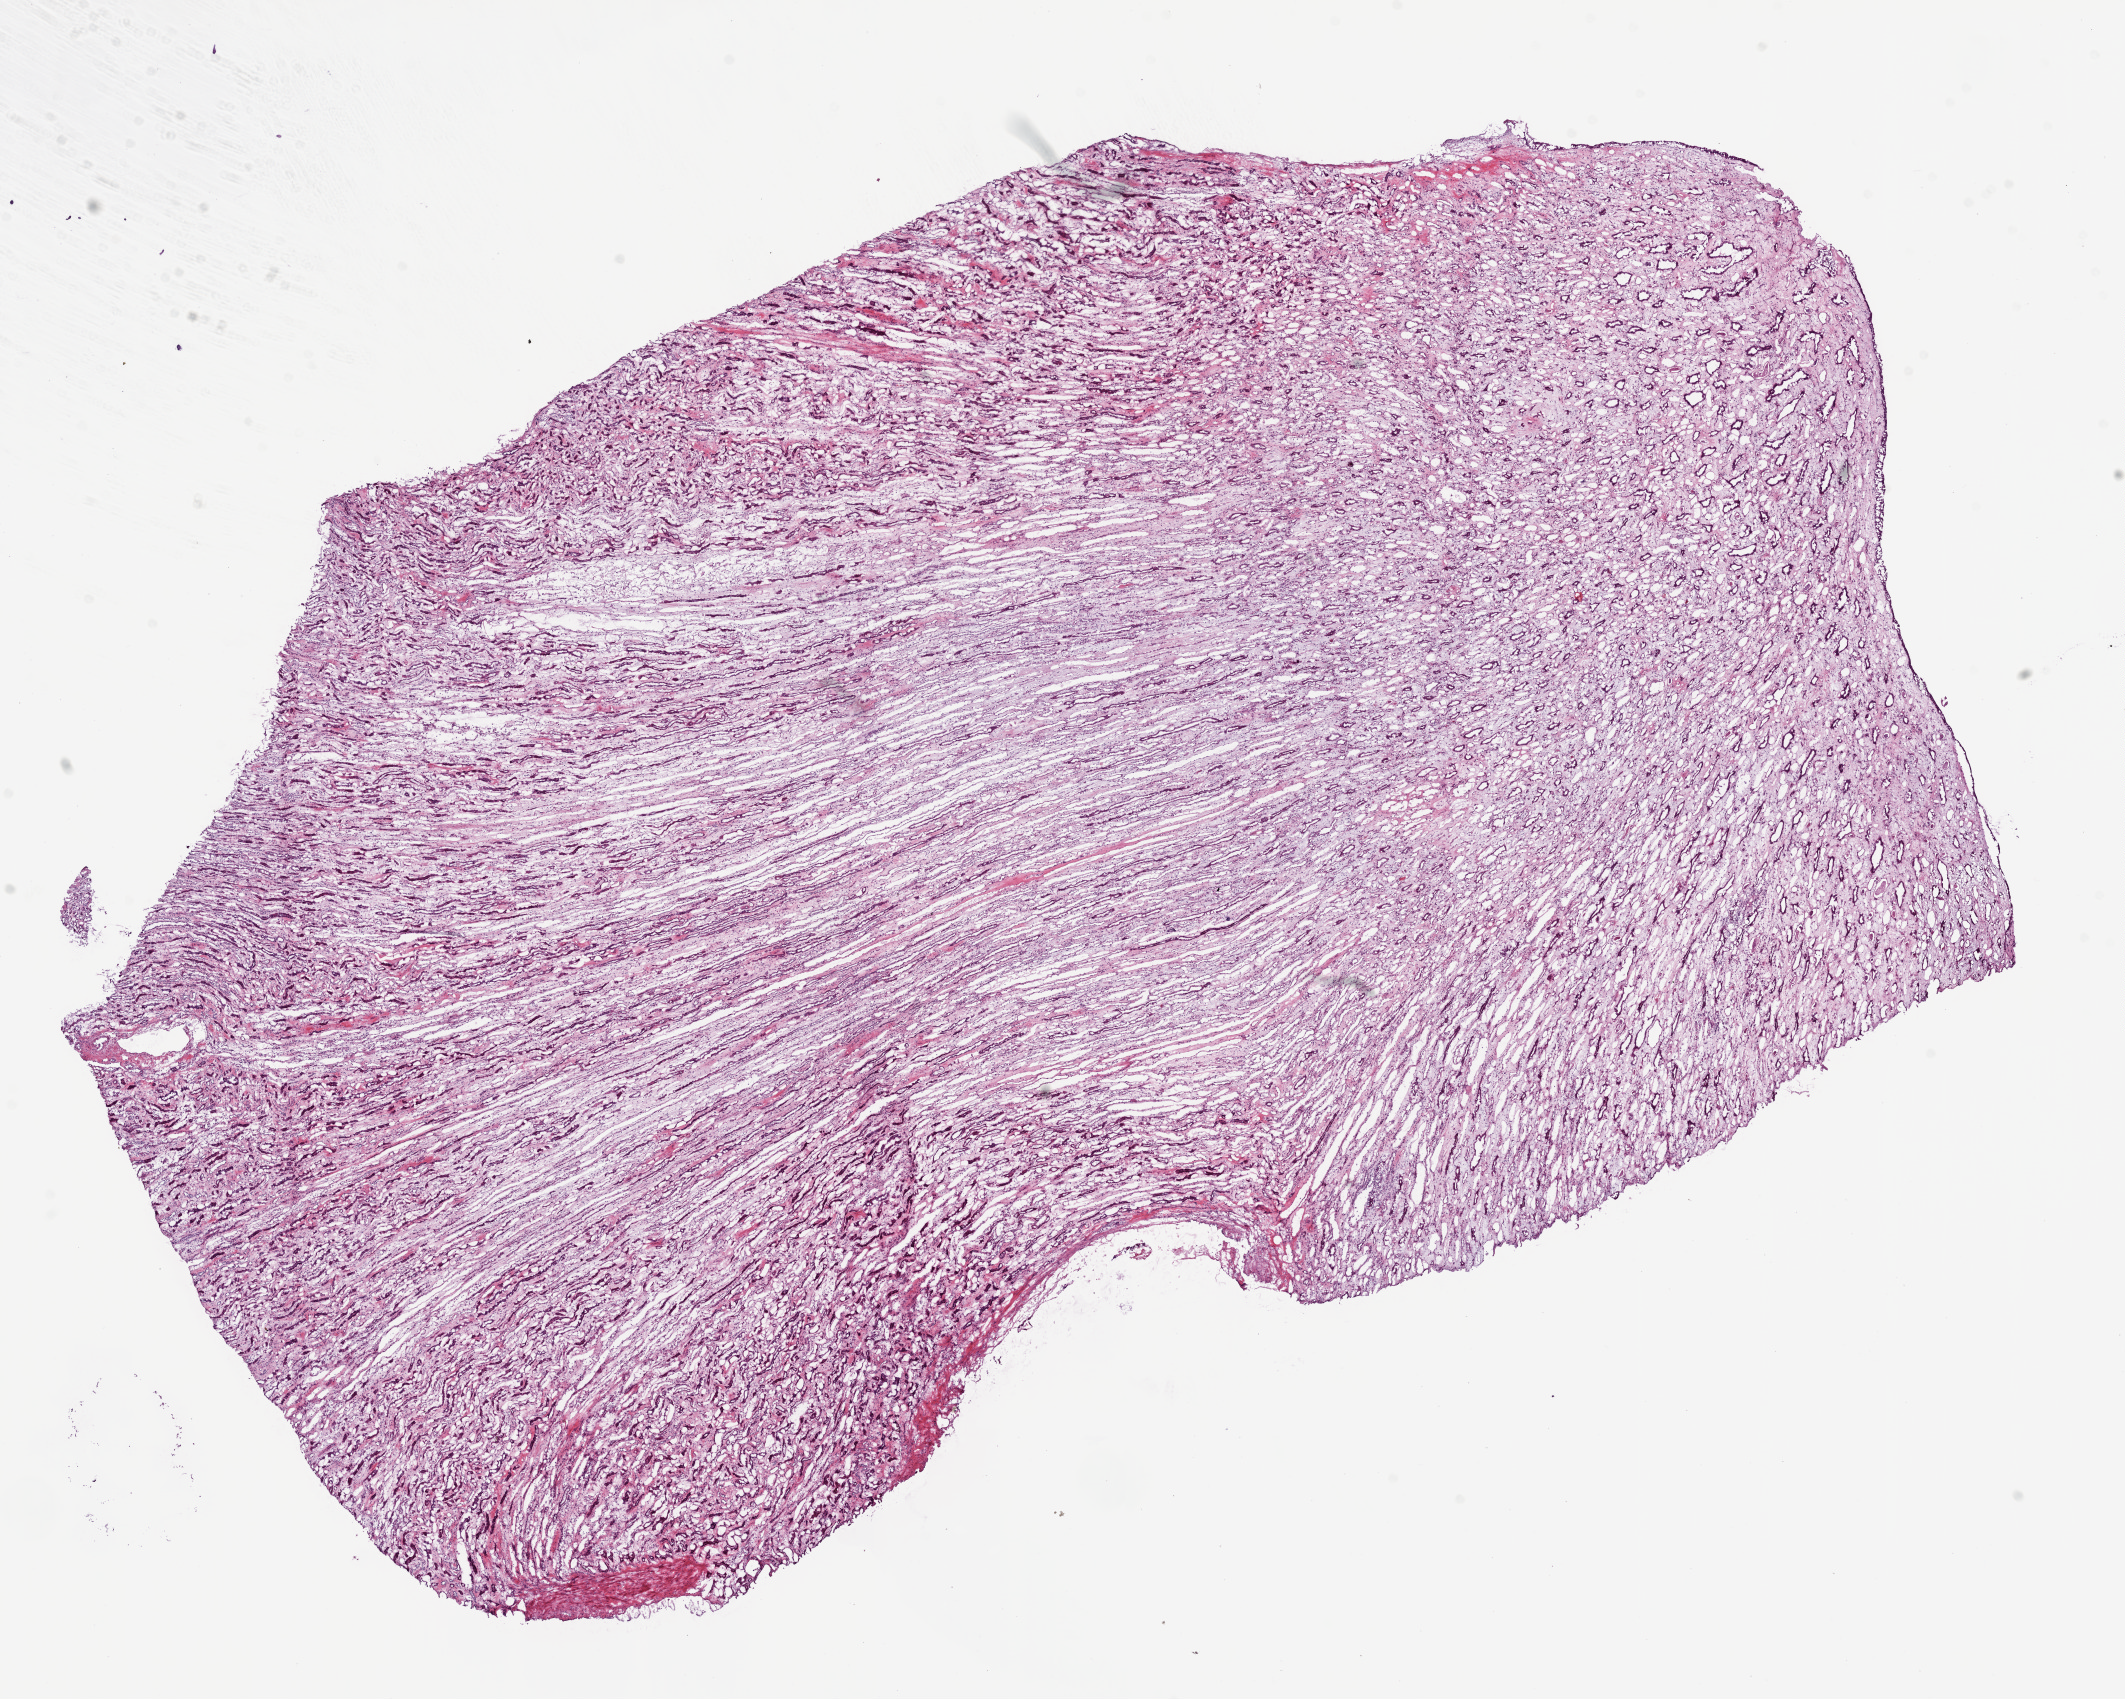
Digitized H&E-stained tissue section (whole slide) — a low-resolution overview of the entire scanned area, about 17.1 x 13.6 mm (slide scanned at 20x); frozen section; kidney, solid tissue normal (non-tumour tissue) sample. Male, age 56 years at initial diagnosis.
This section: solid tissue normal (non-tumour) sample from the same patient. Patient diagnosis: Clear cell adenocarcinoma, NOS.